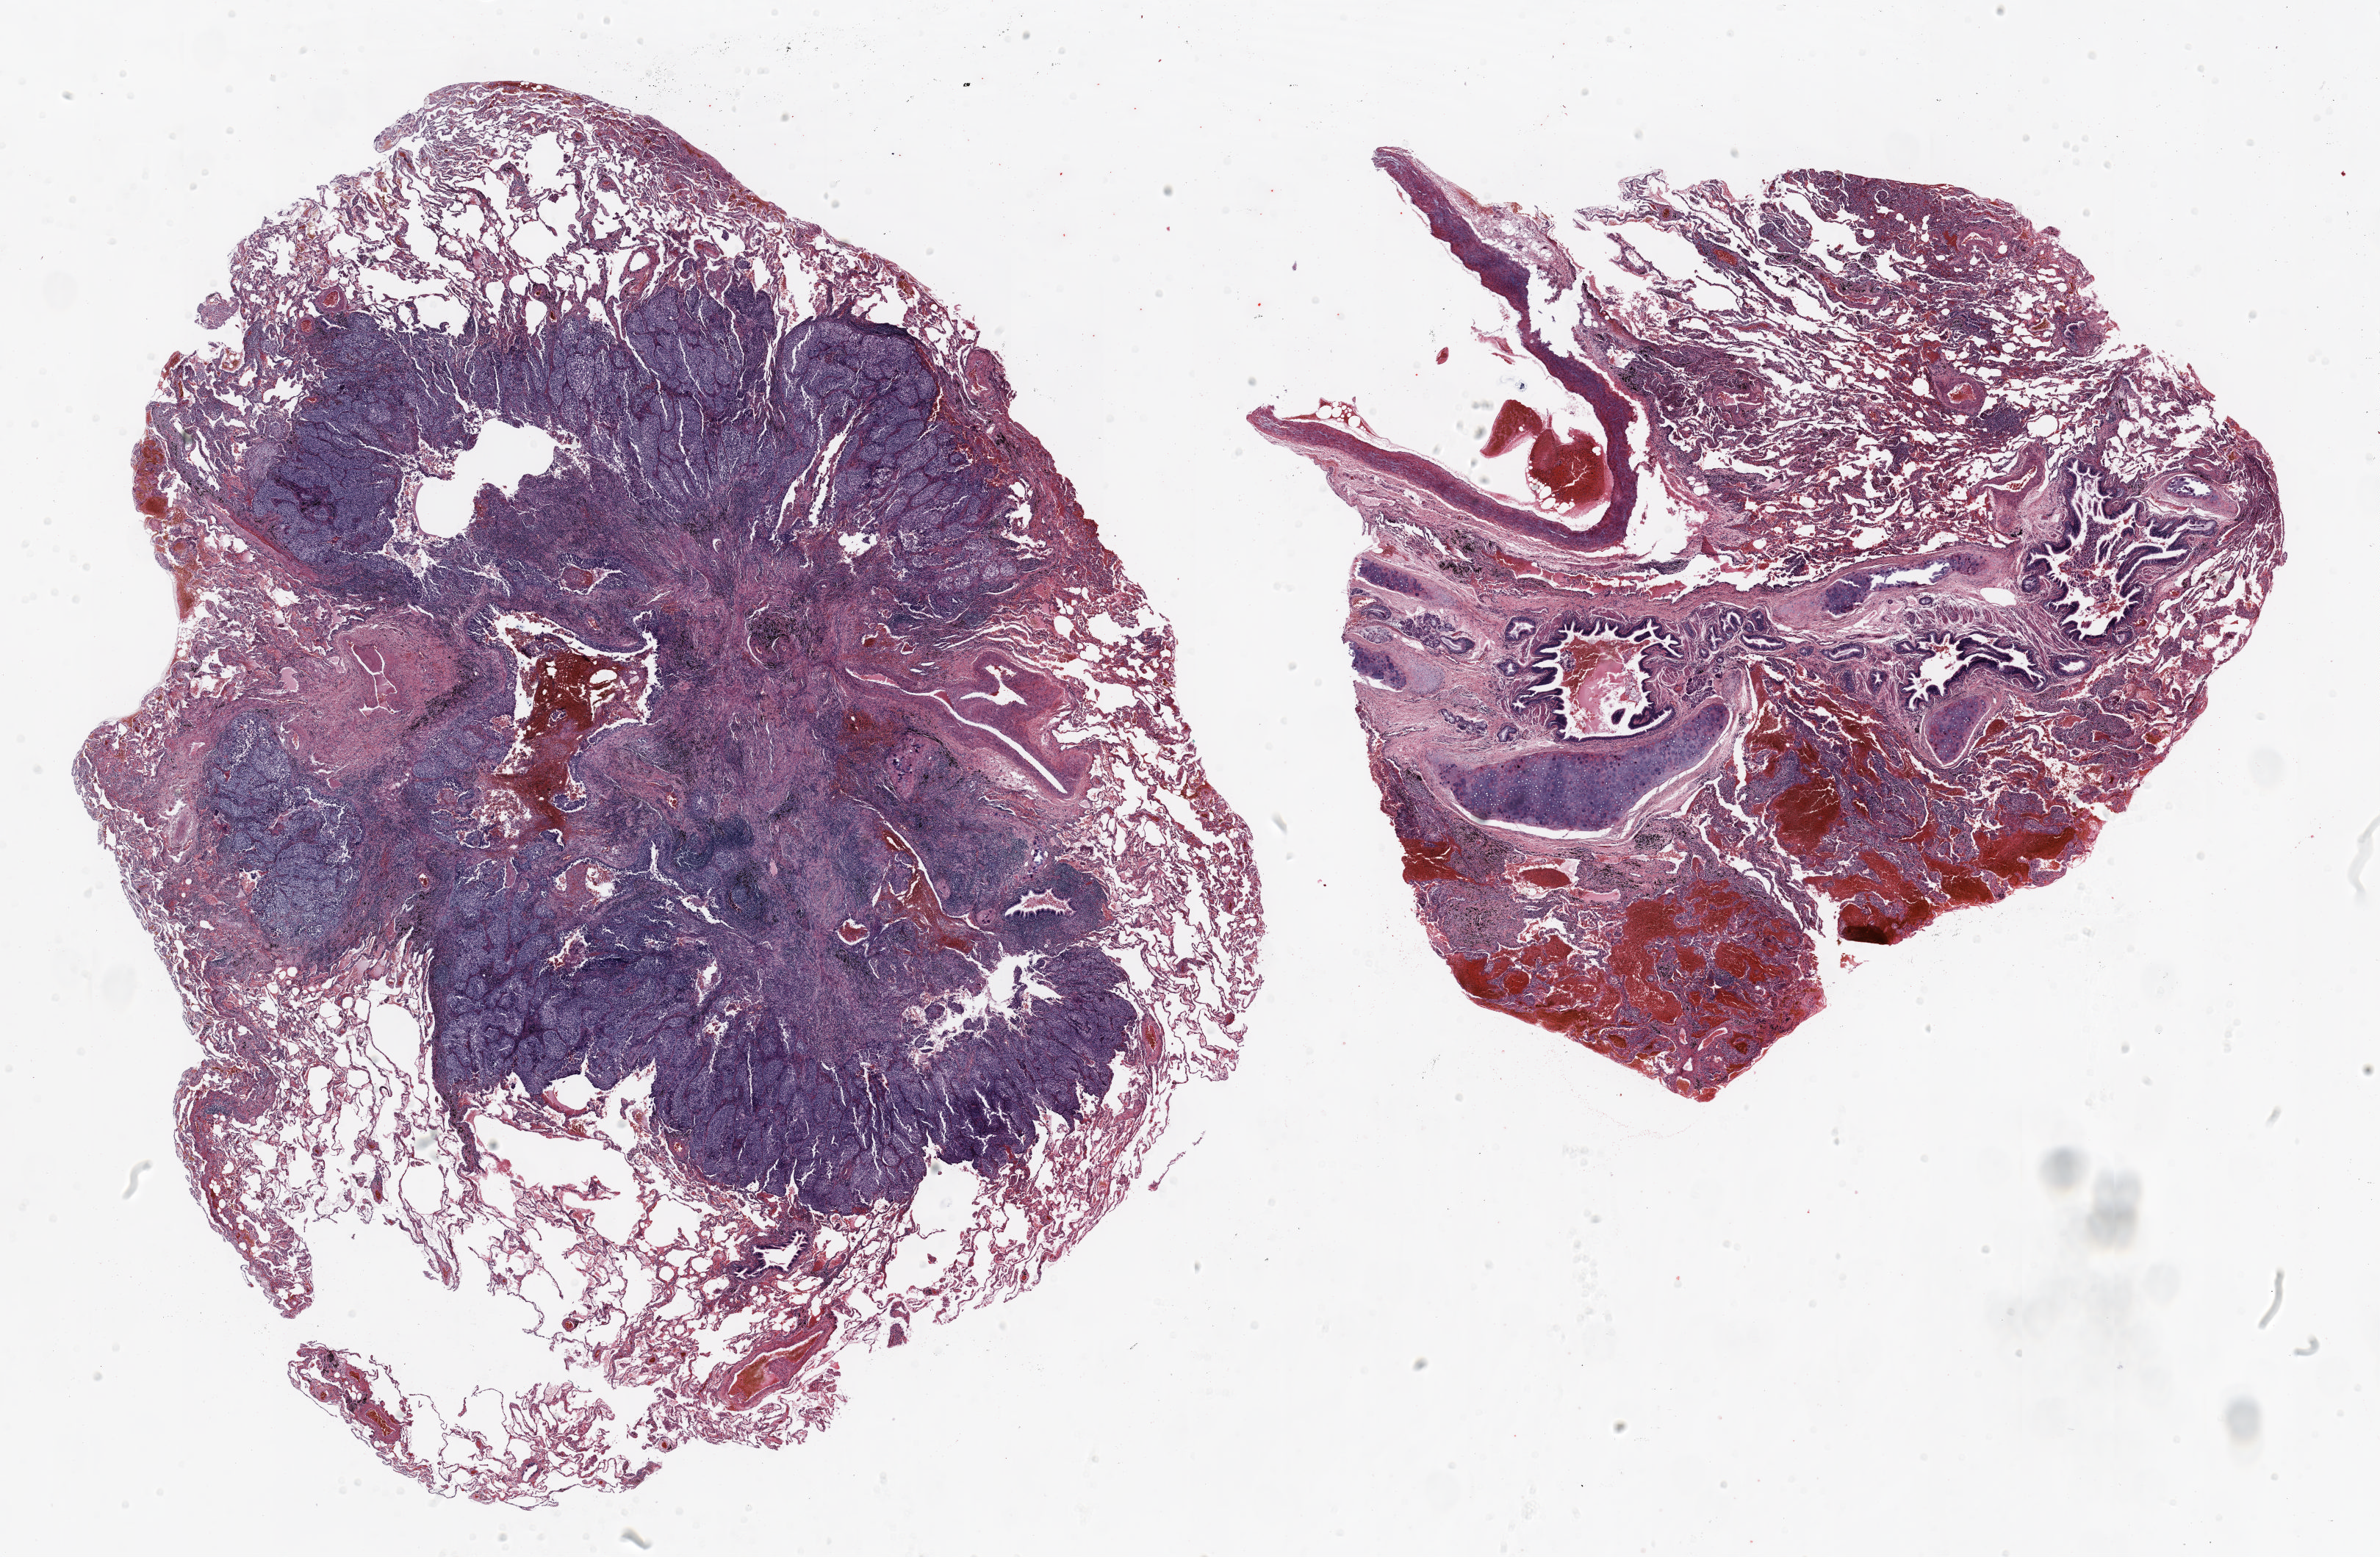
H&E-stained whole-slide image, whole scanned area (about 26.0 x 17.0 mm) shown as a low-resolution overview; formalin-fixed paraffin-embedded (FFPE) section; lung. Female, age 68 at enrolment. Grade: undifferentiated (G4).
- stage (AJCC 6th edition): IA
- participant's lung-cancer diagnosis: Large cell carcinoma, NOS (ICD-O-3 8012/3)
- tumour size (pathology): 10 mm
- primary tumour location (clinical record): left upper lobe